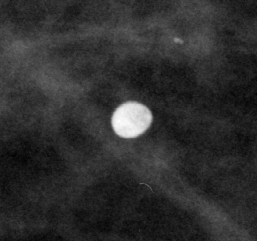
Crop from a digitized film mammogram around one marked abnormality; right breast; CC view.
Finding: calcifications, morphology lucent center; BI-RADS assessment category 2; benign; no additional work-up was recommended (benign without callback).